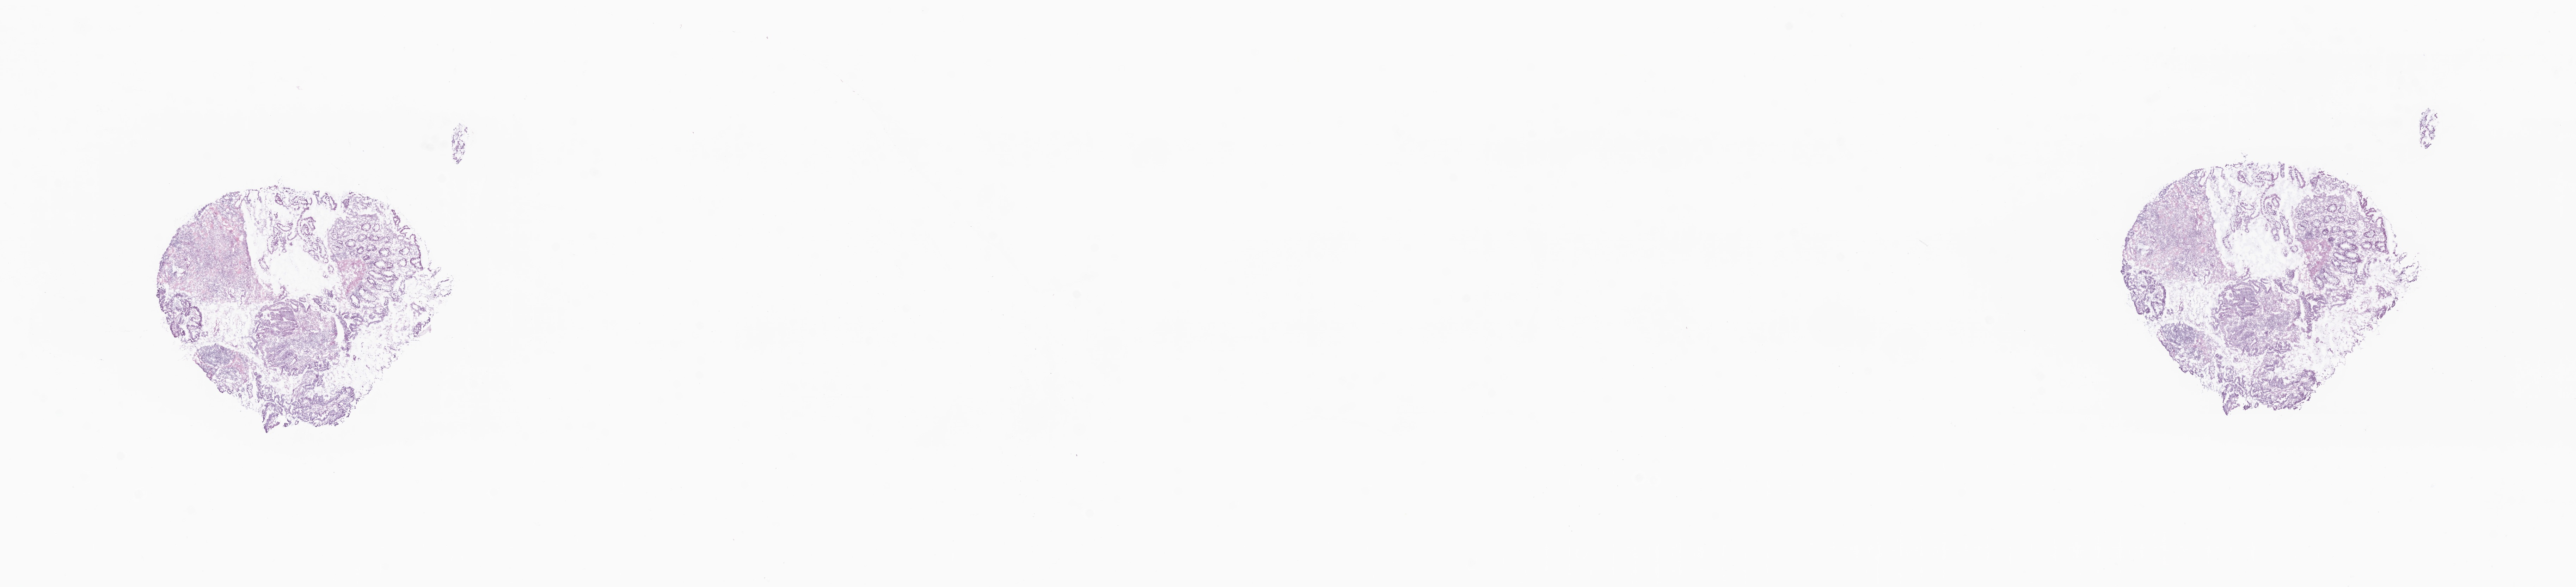
Whole-slide image, H&E stain, whole scanned area (about 30.8 x 7.0 mm) shown as a low-resolution overview; frozen section; primary tumor; site: descending colon. Patient: male, age at initial diagnosis 65 years. Pathologist review of this section (percent, as recorded): tumor cells 50%, tumor nuclei 60%.
Histologic diagnosis: Adenocarcinoma, NOS.